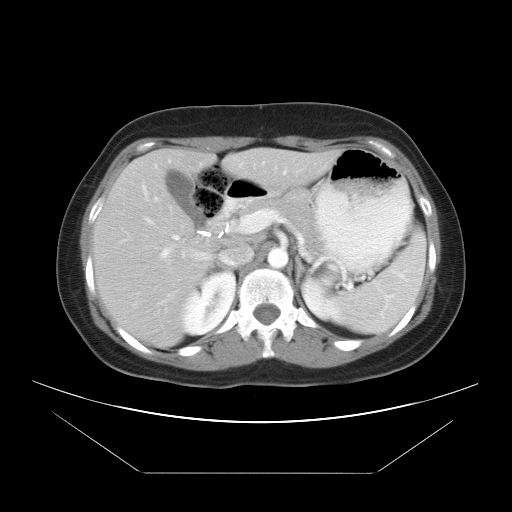
Contrast-enhanced abdominal CT, one axial slice. Slice 24 of 34 in the series (ordered by position). Soft-tissue window (W 400 / L 40 HU). 7.5 mm slice thickness. 512 × 512 image matrix, field of view 410 × 410 mm. Female patient, age 38 years. Case-level facts recorded for this patient, not image findings: diagnosis: colorectal cancer liver metastases, imaged before liver resection.
Structures marked on this image (manually delineated by an expert):
- liver: box from (x=91, y=148) to (x=340, y=347) px
- planned liver remnant (the part of the liver to remain after resection): (x=201, y=148)–(x=341, y=251)
- portal vein (with intrahepatic branches): (x=145, y=172)–(x=285, y=263)